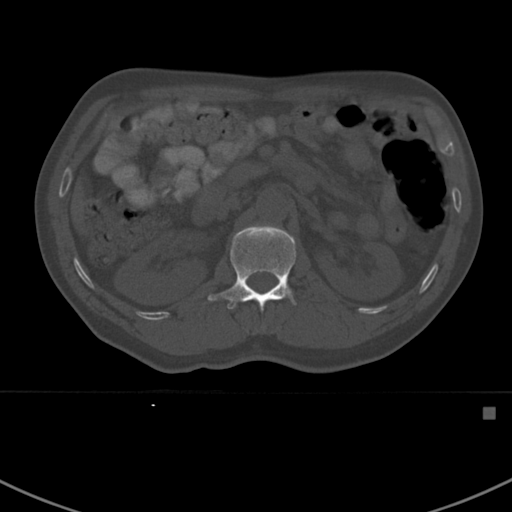
CT including the spine, one axial slice. Slice 308 of 412 in the series (ordered by position). Reconstruction kernel Br40s. Bone window (W 1800 / L 400 HU). 512 × 512 image matrix, field of view 358 × 358 mm. Male patient, age 59 years. From the clinical record (not read from this slice): primary cancer: prostate.
Annotated regions visible in this slice (semi-automatically segmented with operator editing):
- L1 vertebra: box from (x=208, y=224) to (x=297, y=313) px